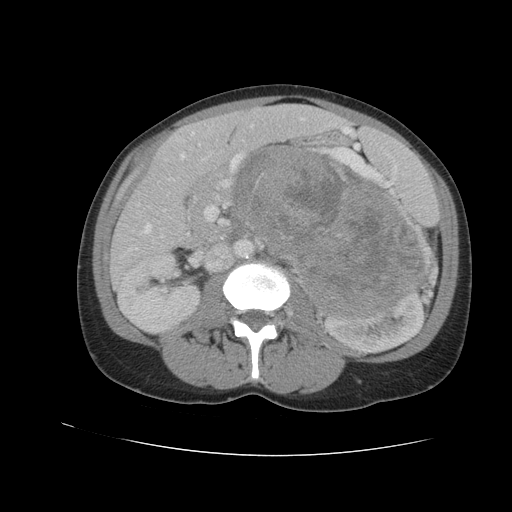
Contrast-enhanced abdominal CT, one axial slice. Position 56 of 90 along the scan axis. Reconstruction kernel STANDARD. 120 kVp. Intravenous contrast given. Soft-tissue window (W 400 / L 40 HU). 512 × 512 image matrix, field of view 360 × 360 mm. Female patient. From the clinical record (not read from this slice): diagnosis: adrenocortical carcinoma; tumour side: left adrenal; tumour size at pathology: 18 cm; Ki-67 index: 11 %; stage (as recorded): 3.
Structures marked on this image (semi-automatic segmentation, software-assisted and operator-edited):
- mass: bounding box [x1, y1, x2, y2] px = [238, 147, 424, 314]